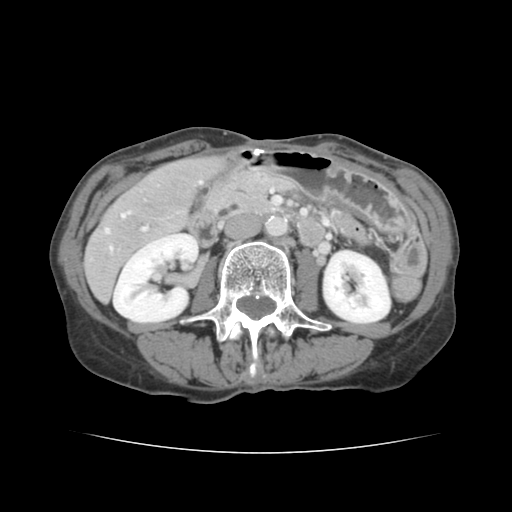
Contrast-enhanced abdominal CT, one axial slice. Position 48 of 136 along the scan axis. Intravenous contrast given. Soft-tissue window (W 400 / L 40 HU). 2.5 mm slice thickness. 512 × 512 image matrix, field of view 319 × 319 mm. Female patient, age 77 years. From the clinical record (not read from this slice): diagnosis: colorectal cancer liver metastases, imaged before liver resection; multiple liver metastases: yes; largest metastasis: 3 cm; disease in both lobes: no.
Outlined on this slice (outlined manually by an expert reader):
- hepatic veins: bounding box (x1, y1, x2, y2) in pixels: (105, 181, 201, 250)
- liver: (86, 157, 218, 300)
- planned liver remnant (the part of the liver to remain after resection): (170, 158, 220, 192)
- portal vein (with intrahepatic branches): (142, 227, 147, 231)